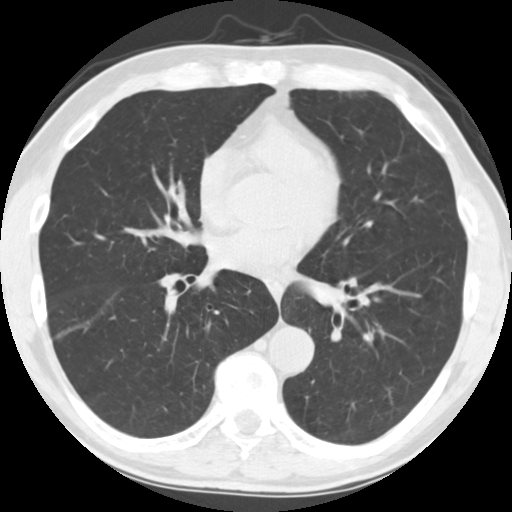
Axial slice from a low-dose chest CT screening exam, second annual screen, lung window (W 1500 / L -600 HU), 2.5 mm slice thickness, 120 kVp, slice 108 of 245 in the series. Male, age 64 years at enrolment. Current smoker at enrolment.
Expert-annotated lung lesion, bounding box (x1, y1, x2, y2) in pixels: (354, 320, 390, 348). Screening reader's record for this exam: no non-calcified nodule ≥4 mm recorded. Participant outcome: lung cancer diagnosed 561 days after this screen (after the third annual screen) — adenocarcinoma, NOS, left lower lobe, stage IV (AJCC 6th edition), 44 mm at pathology.